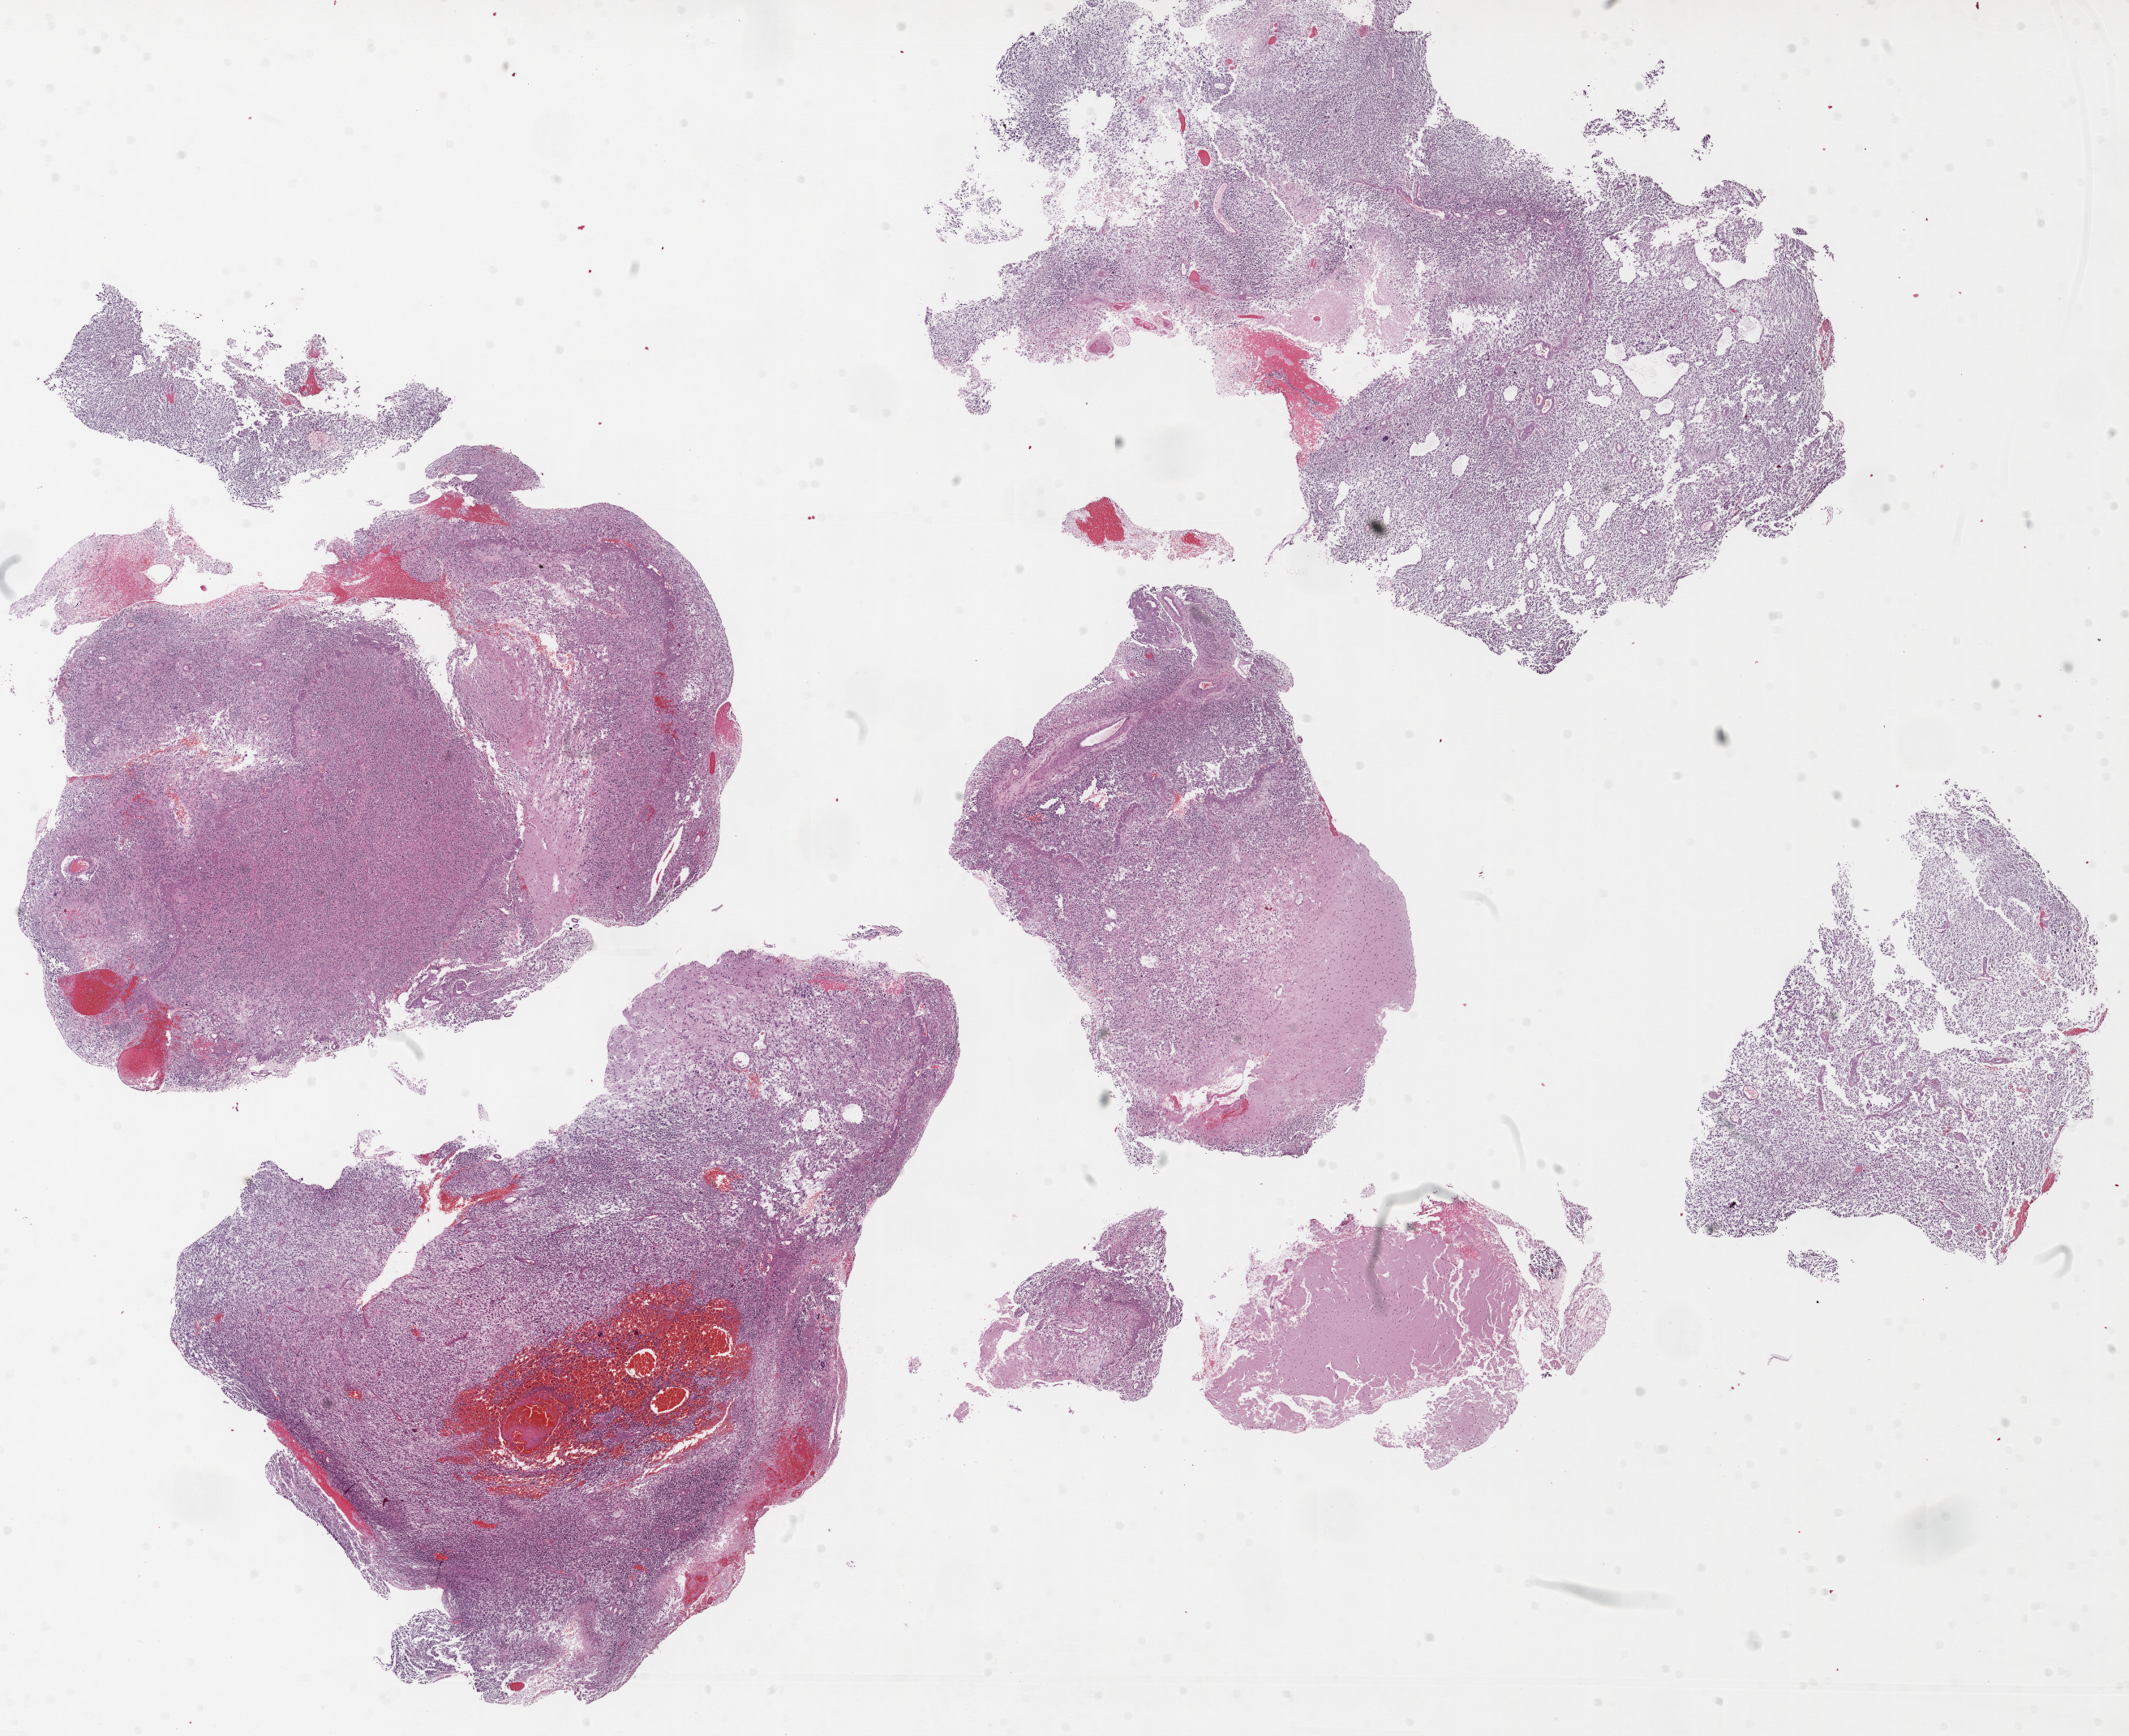
H&E-stained whole-slide image, shown as a low-resolution overview of the whole scanned area (about 21.1 x 17.2 mm, from a 20x scan). Formalin-fixed paraffin-embedded (FFPE) diagnostic section. Sample: primary tumour, brain. Female, age 54 years at initial diagnosis.
* diagnosis: Glioblastoma